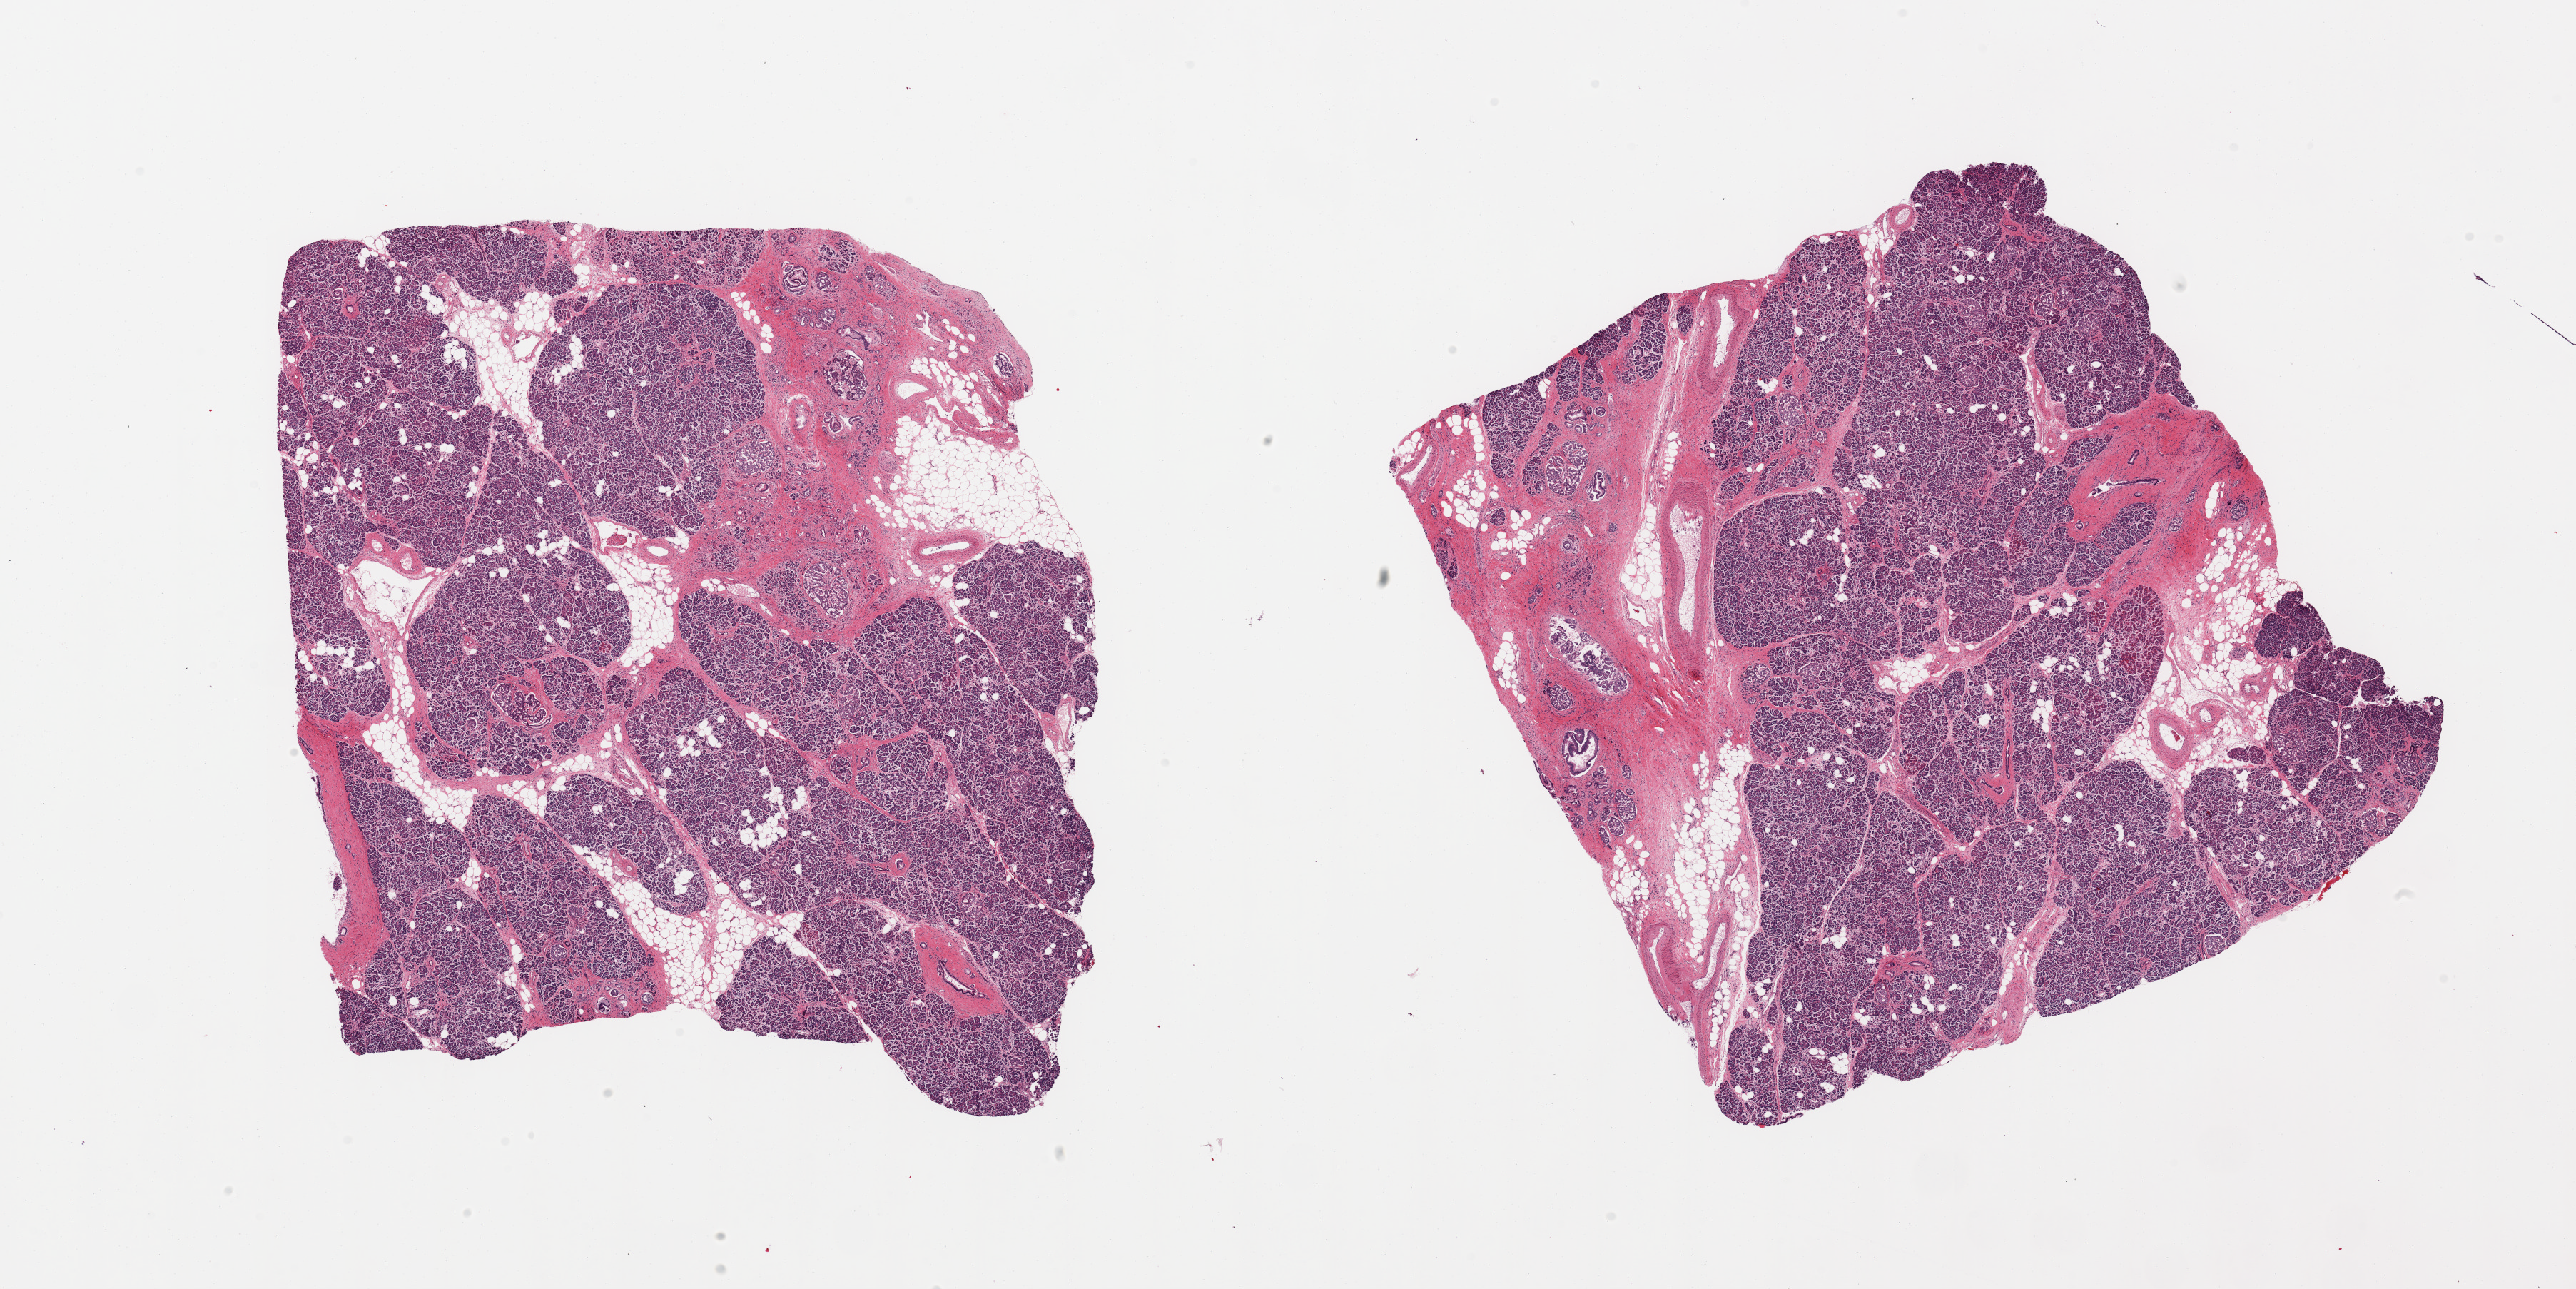
H&E whole-slide image, shown as a low-resolution overview of the whole scanned area (about 28.5 x 14.3 mm), PAXgene-fixed paraffin-embedded (PFPE) section, sampled site (target tissue): pancreas, donor tissue sample.
Pathologist's review note for this sample: 2 pieces, moderate autolysis; Islets still visible but starting to degrade noticeably.